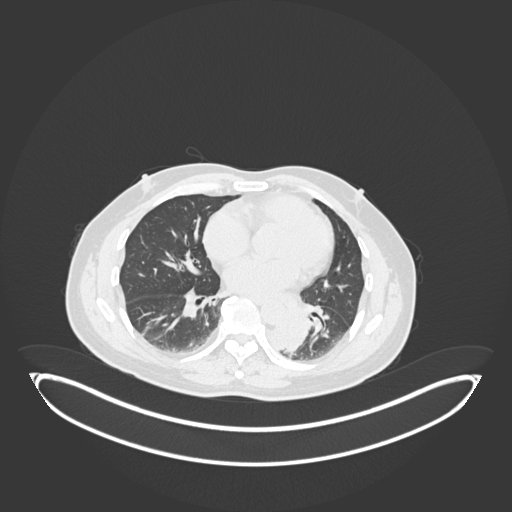
Chest CT, one axial slice. Position 80 of 258 along the scan axis. Reconstruction kernel B30f. 120 kVp. Lung window (W 1500 / L -600 HU). 1 mm slice thickness. 512 × 512 image matrix, field of view 500 × 500 mm. Patient: male, 54 years. From the clinical record (not read from this slice): clinical TNM (as recorded): T3 N0 M0.
Outlined on this slice (bounding box drawn by a radiologist):
- lung tumour (recorded histology: squamous cell carcinoma): box from (x=265, y=307) to (x=313, y=356) px